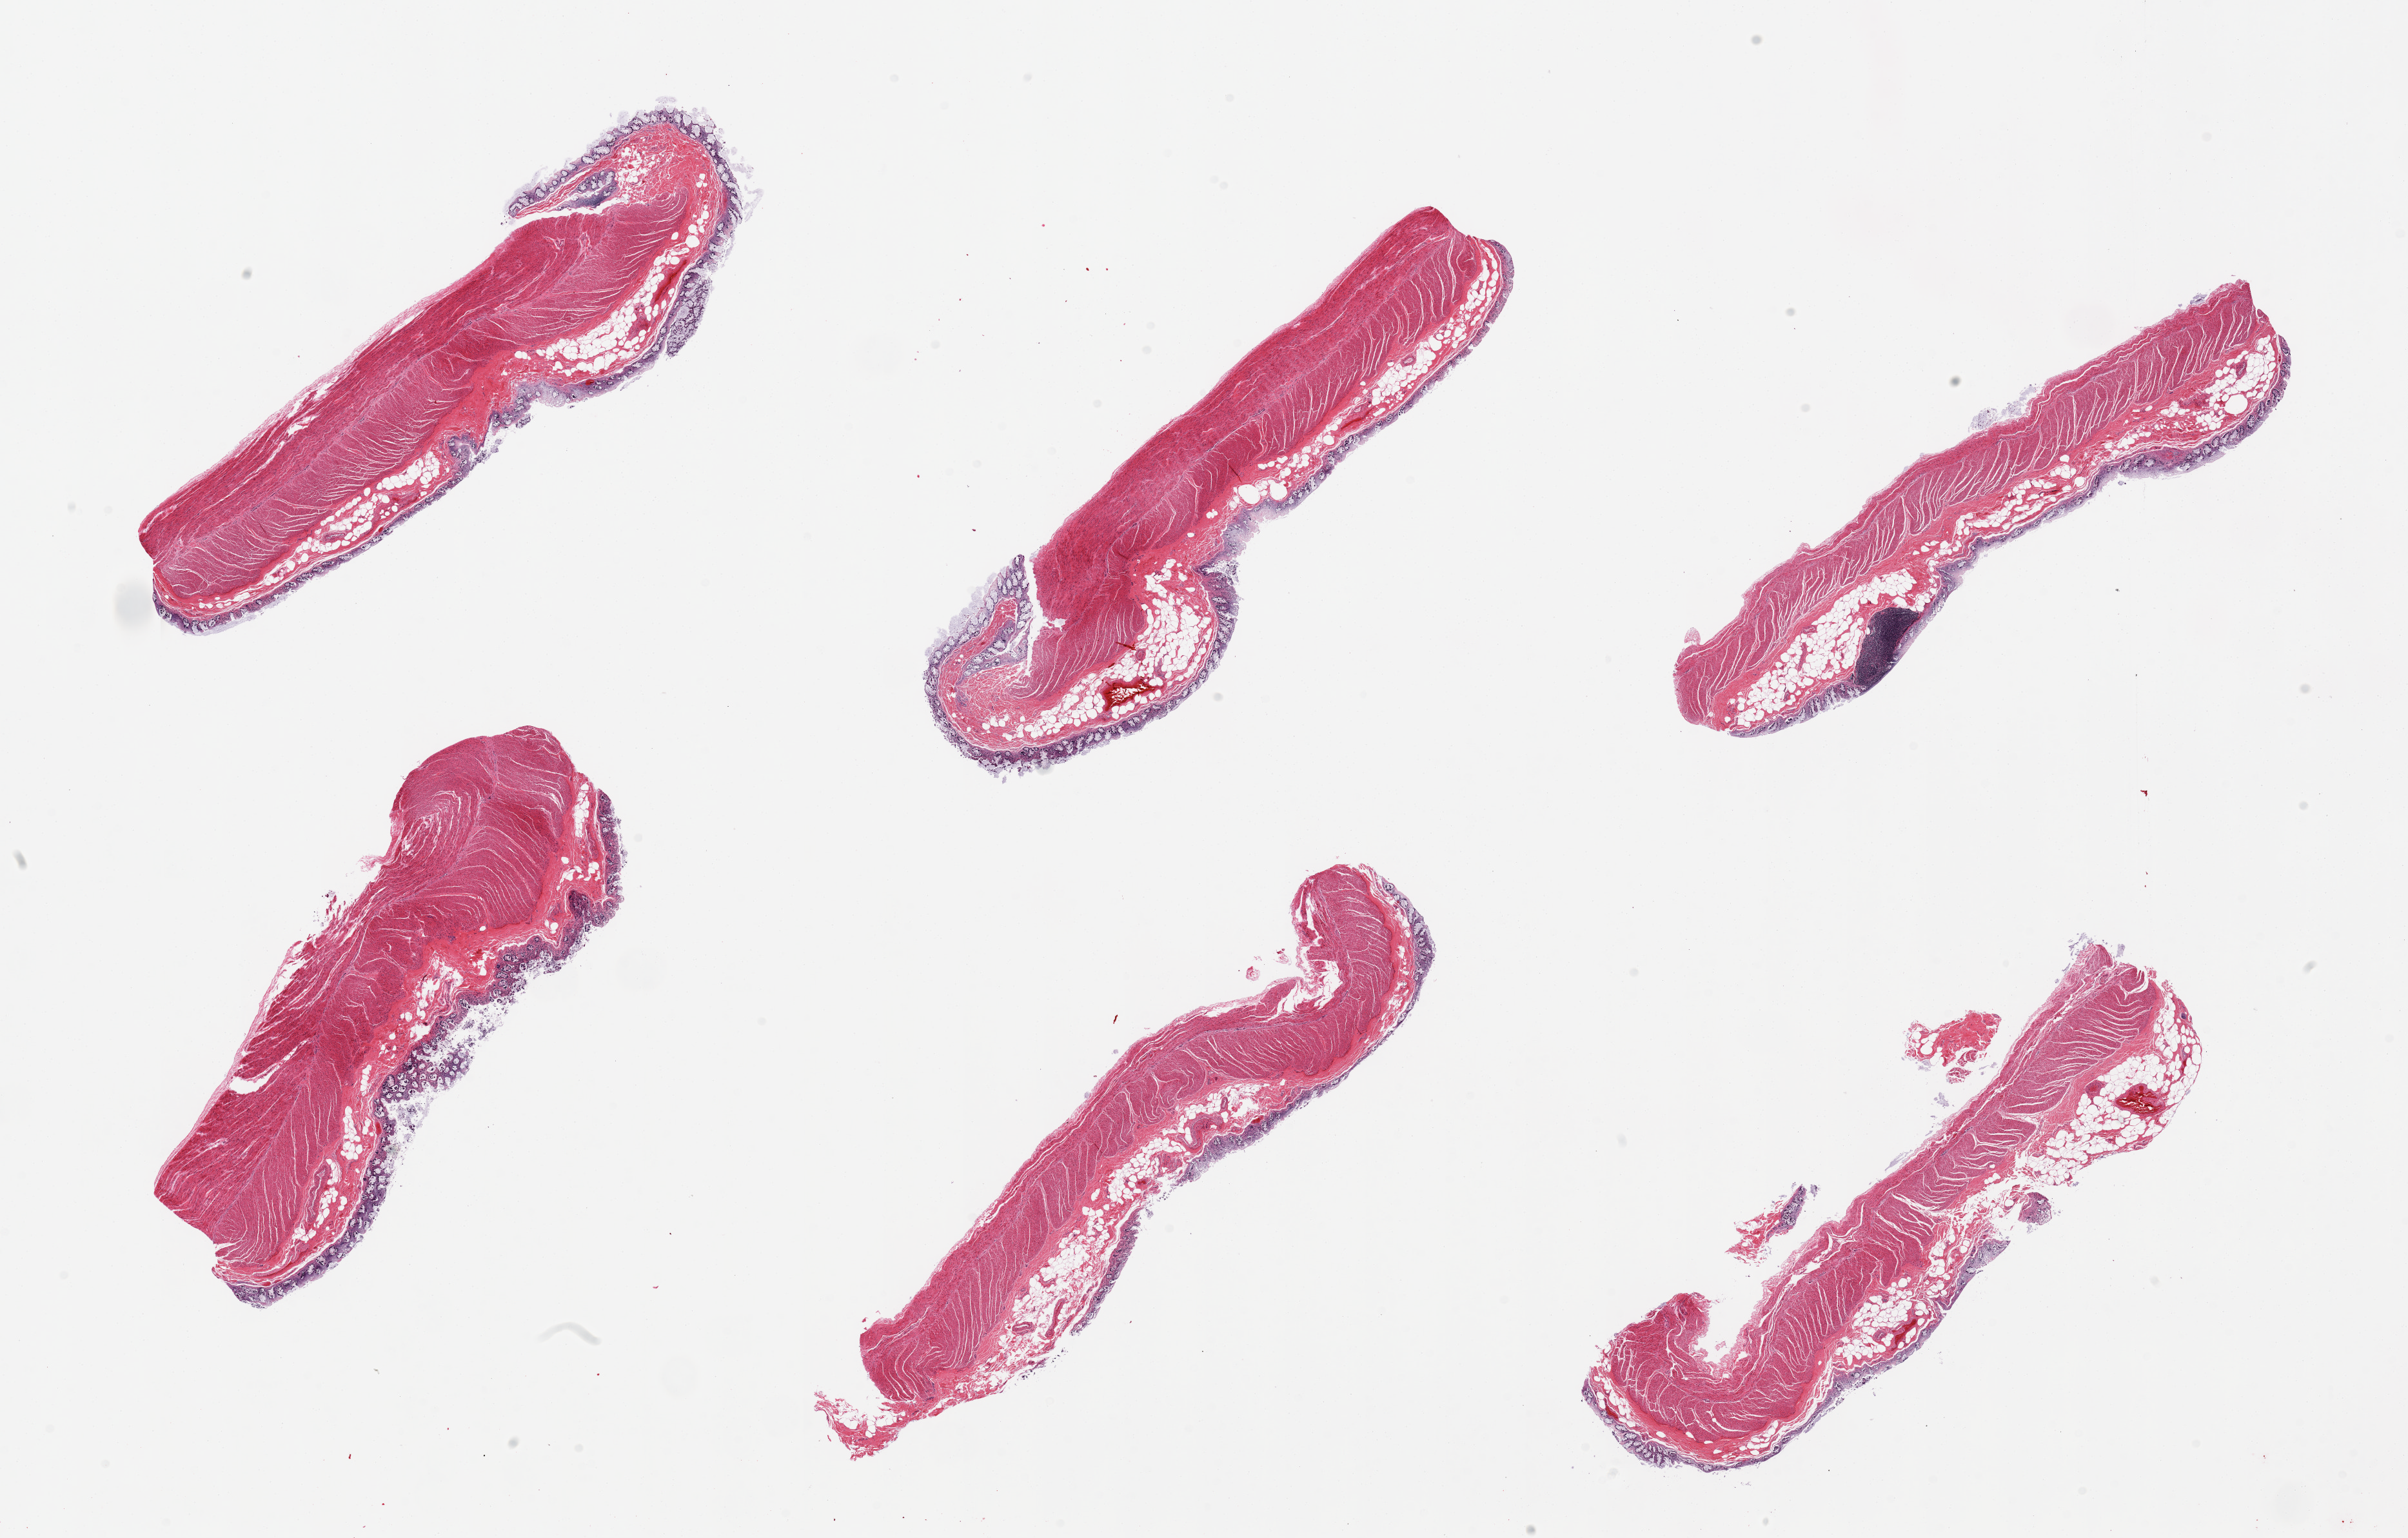
Whole-slide image, H&E stain, brightfield, a low-resolution overview of the entire scanned area, about 29.5 x 18.9 mm. PAXgene-fixed, paraffin-embedded tissue. Sampled site (target tissue): transverse colon. Donor tissue sample. Male donor.
Review note (as recorded): 6 pieces, mucosa markedly autolyzed, ~10-15% thickness.